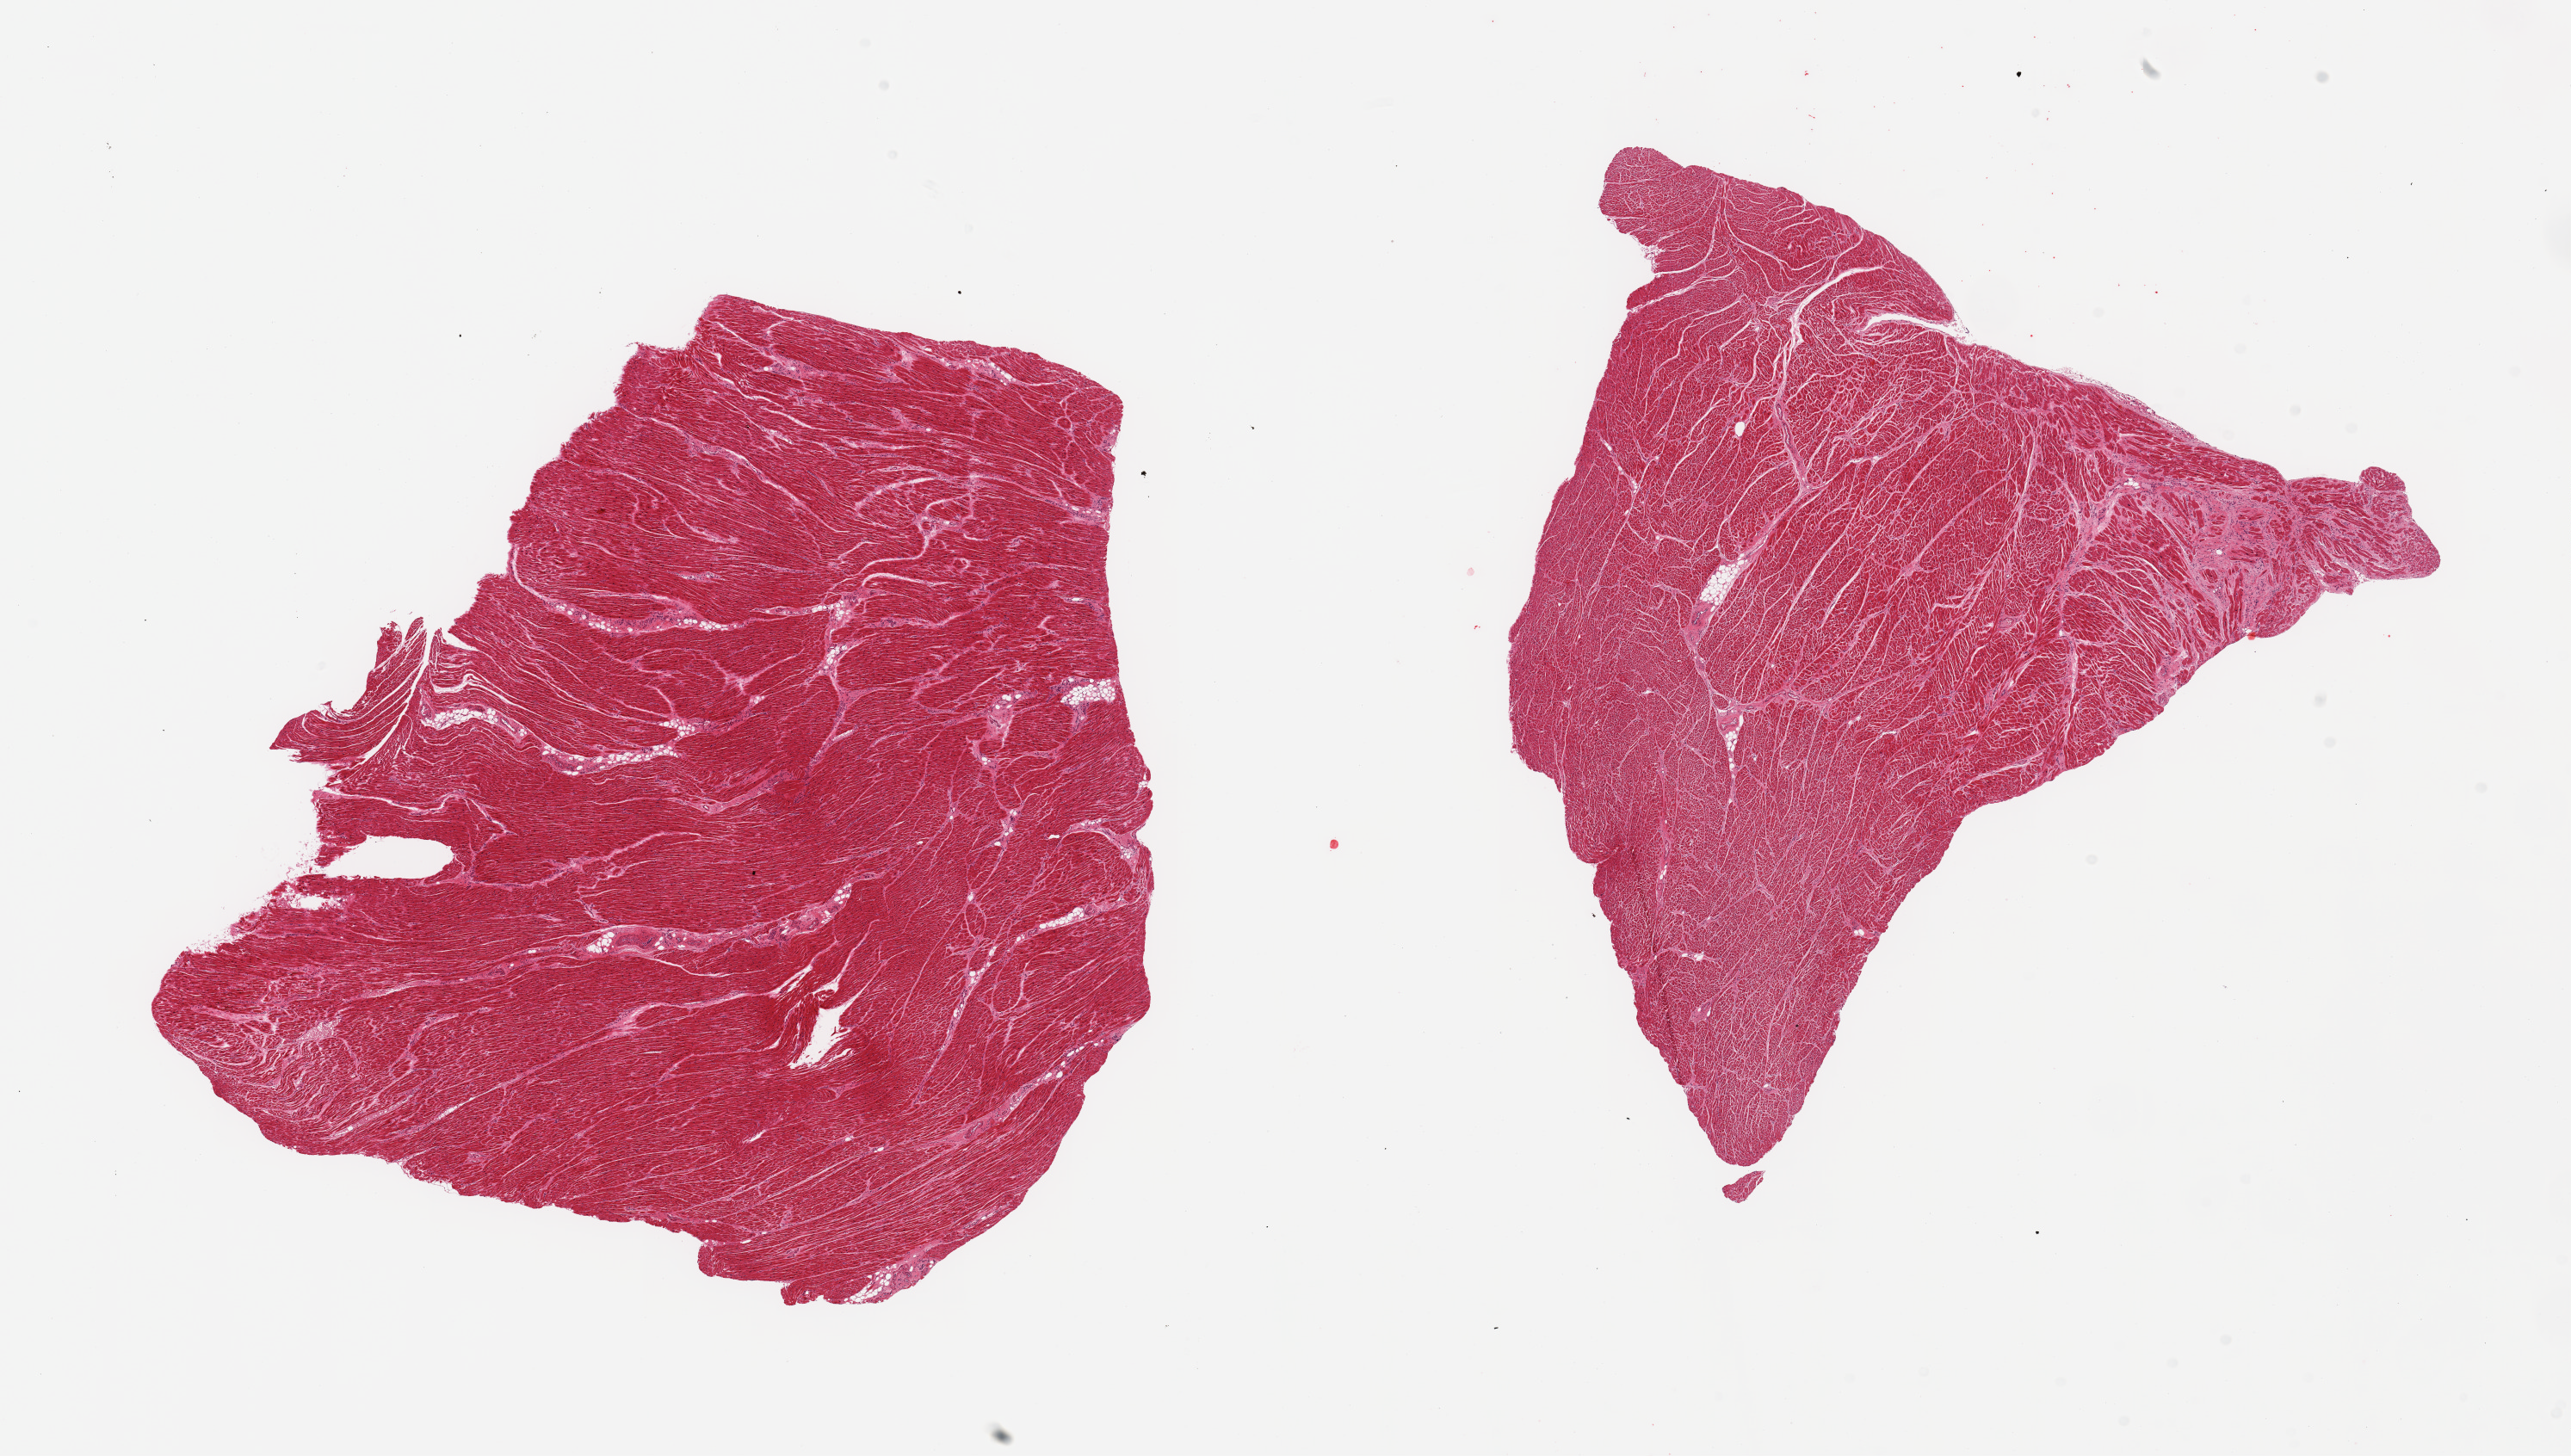
Haematoxylin and eosin whole-slide image, a low-resolution overview of the entire scanned area, about 23.6 x 13.4 mm. PAXgene-fixed, paraffin-embedded tissue. Section of heart (target tissue). Donor tissue sample. Female donor.
Pathologist's review note for this sample: 2 pieces; 1.5mm area of fibrous scar.